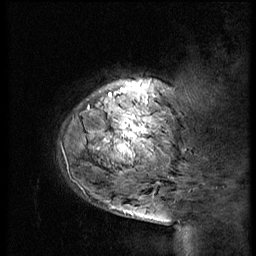
Breast MRI (dynamic contrast-enhanced), one sagittal slice. Position 10 of 56 along the scan axis. 3 images stored at this slice position (order not interpretable as contrast timing). 1.5 T. TE 4.2 ms, TR 9 ms. 2.5 mm slice thickness. 256 × 256 image matrix, field of view 180 × 180 mm. Patient: female, 51 years. Case-level facts recorded for this patient, not image findings: setting: breast cancer imaged before/during neoadjuvant chemotherapy; receptor status: triple-negative.
Annotated regions visible in this slice (semi-automatic segmentation, software-assisted and operator-edited):
- analysis volume of interest (the breast-tissue region the enhancement analysis was run in; not a lesion): bounding box [x1, y1, x2, y2] px = [53, 70, 183, 179]
- tumour enhancement mask (voxels above the 140 % enhancement threshold inside the analysis volume of interest): [96, 94, 145, 153]